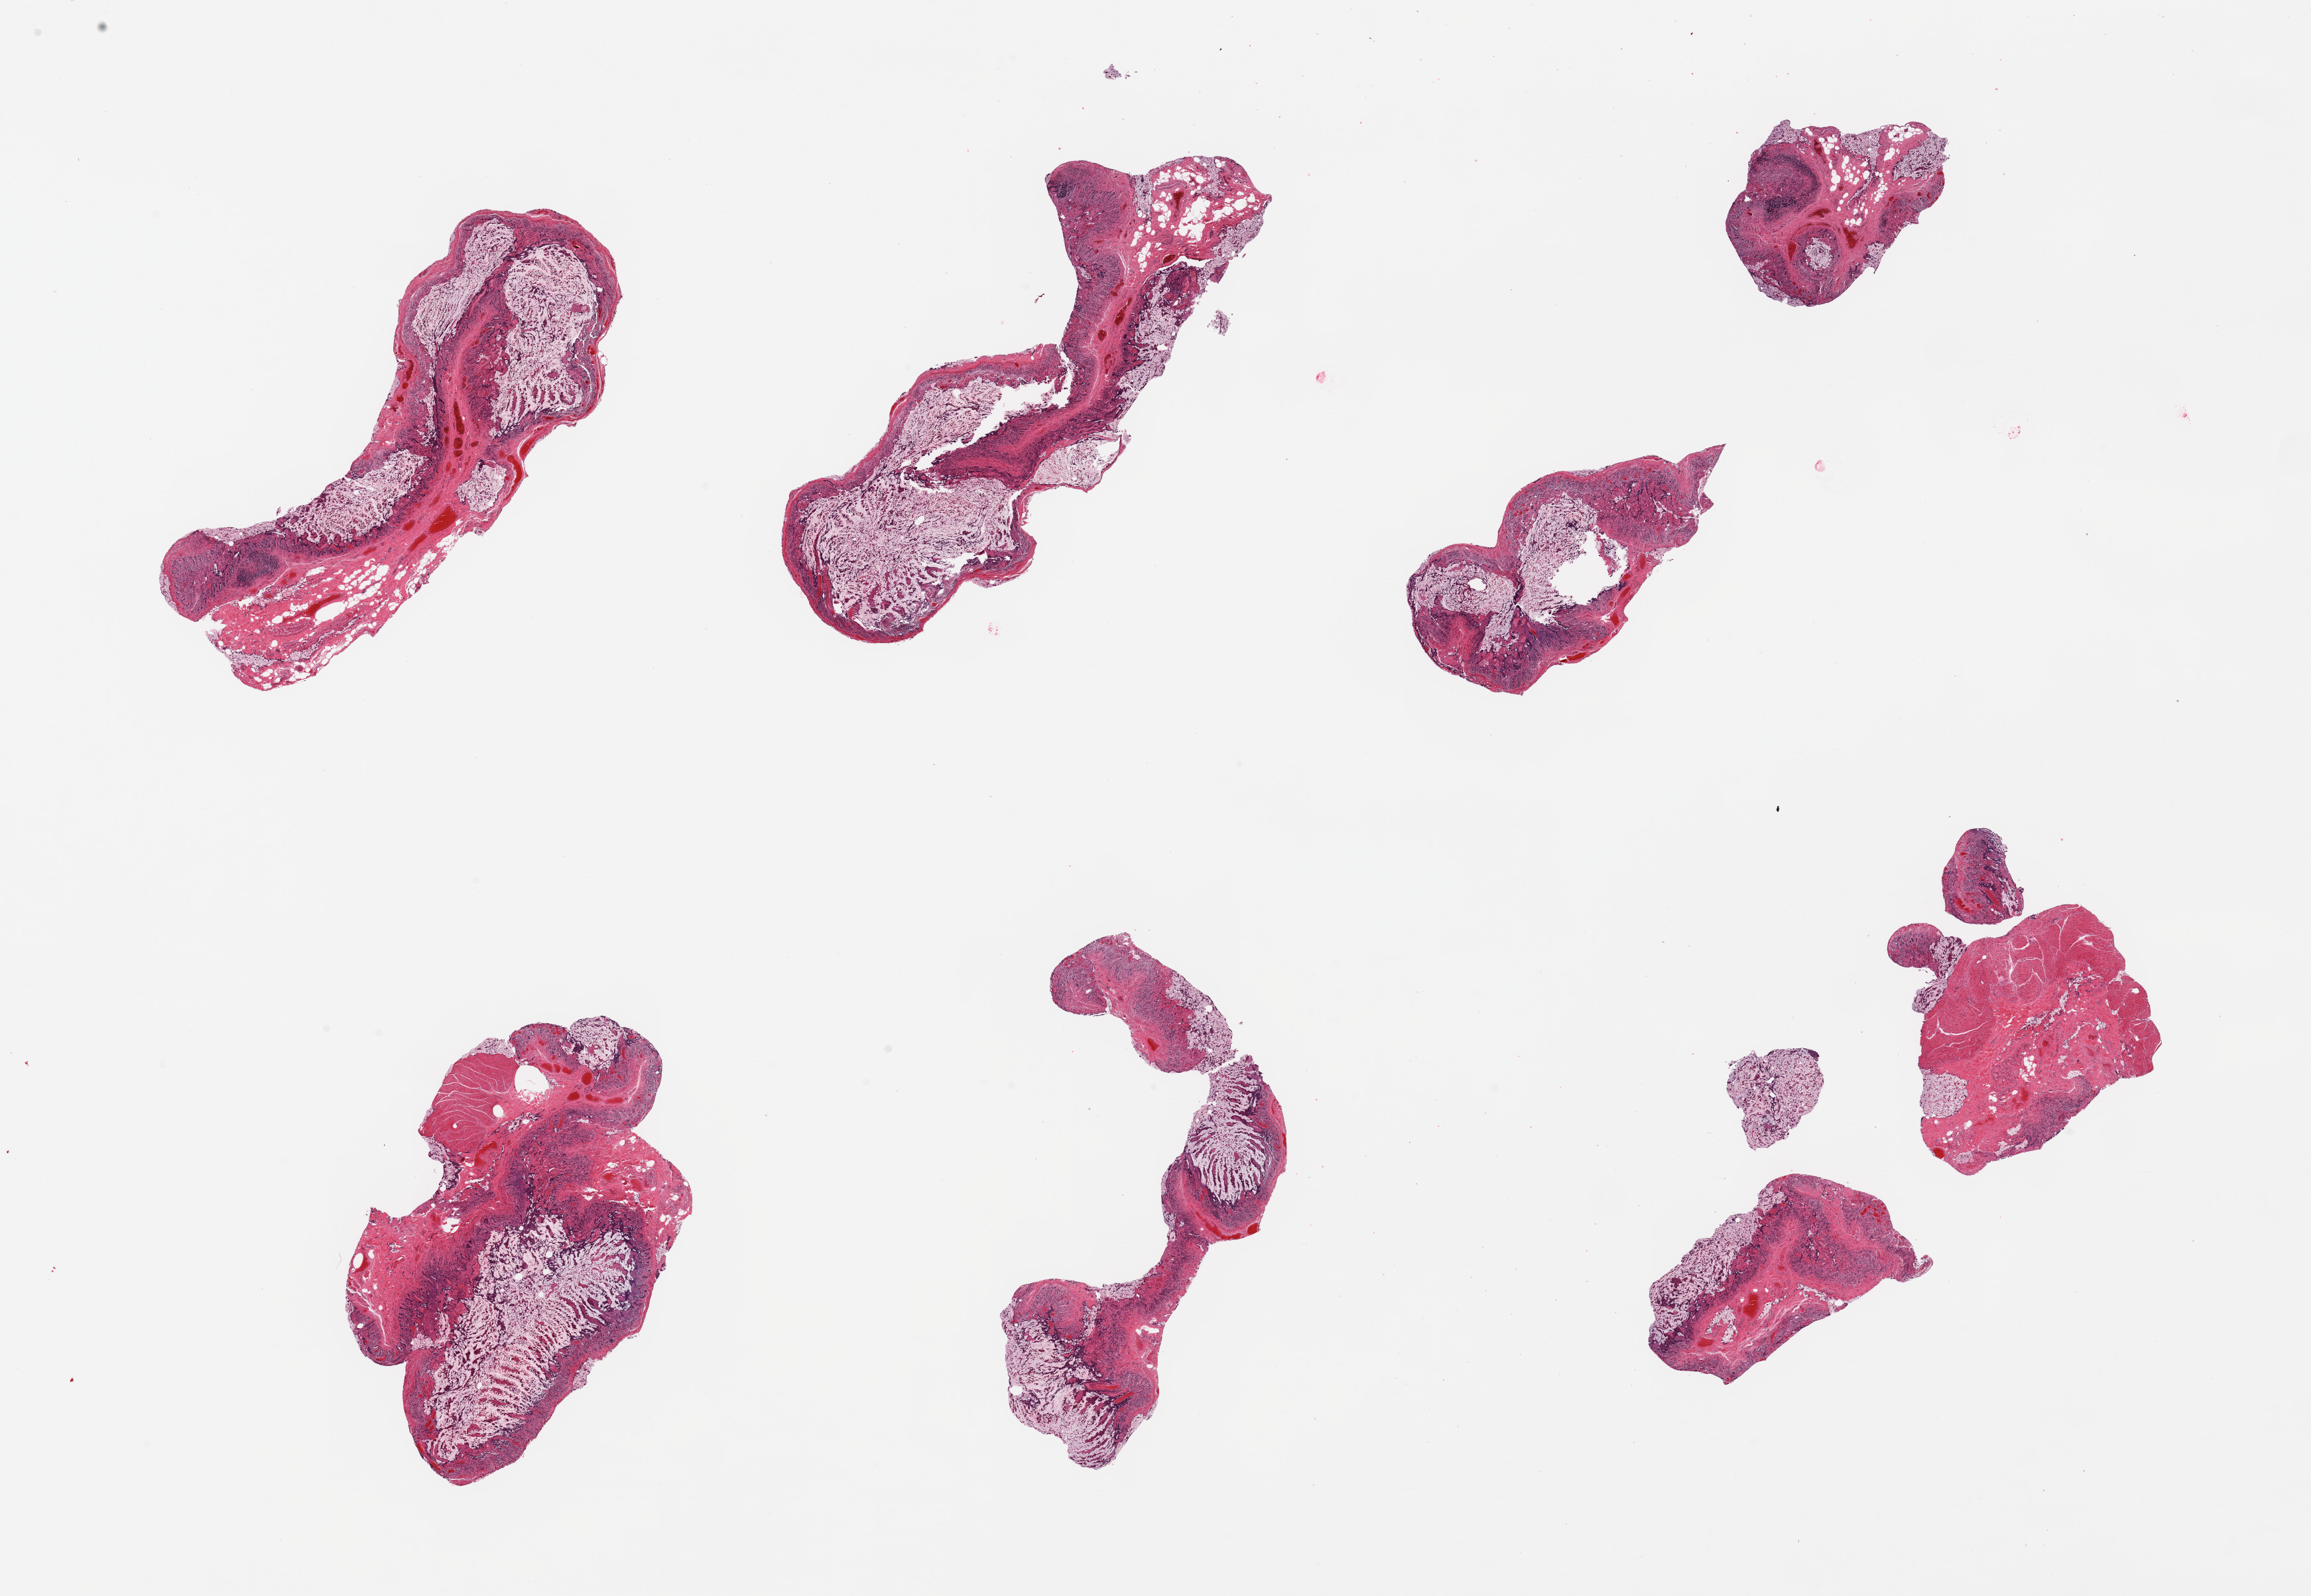
Digitized haematoxylin and eosin-stained section, low-resolution overview of the scanned area, about 27.6 x 19.0 mm (acquisition: 20x scan), PAXgene-fixed paraffin-embedded (PFPE) section, target tissue: ileum, donor tissue sample.
Pathologist's review note for this sample: 6 pieces; too little intact lymphoid tissue.